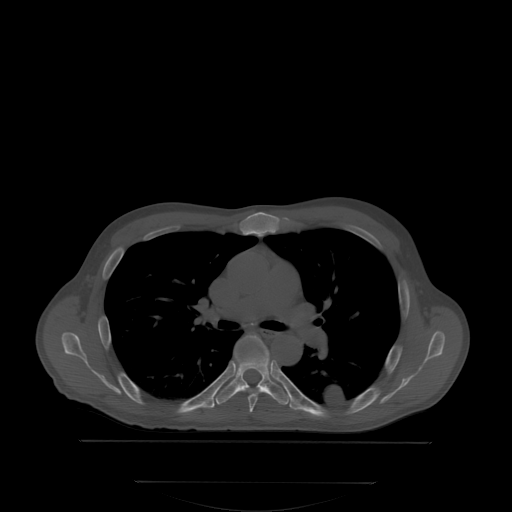
CT including the spine, one axial slice; position 241 of 350 along the scan axis; bone window (W 1800 / L 400 HU); 2.5 mm slice thickness; 512 × 512 image matrix, field of view 500 × 500 mm. Male patient, age 58 years. From the clinical record (not read from this slice): primary cancer: prostate; vertebrae with lytic lesions (as recorded): L1.
Outlined on this slice (semi-automatic segmentation, software-assisted and operator-edited):
- T5 vertebra: bounding box (x1, y1, x2, y2) in pixels: (249, 389, 260, 412)
- T6 vertebra: (215, 336, 291, 404)